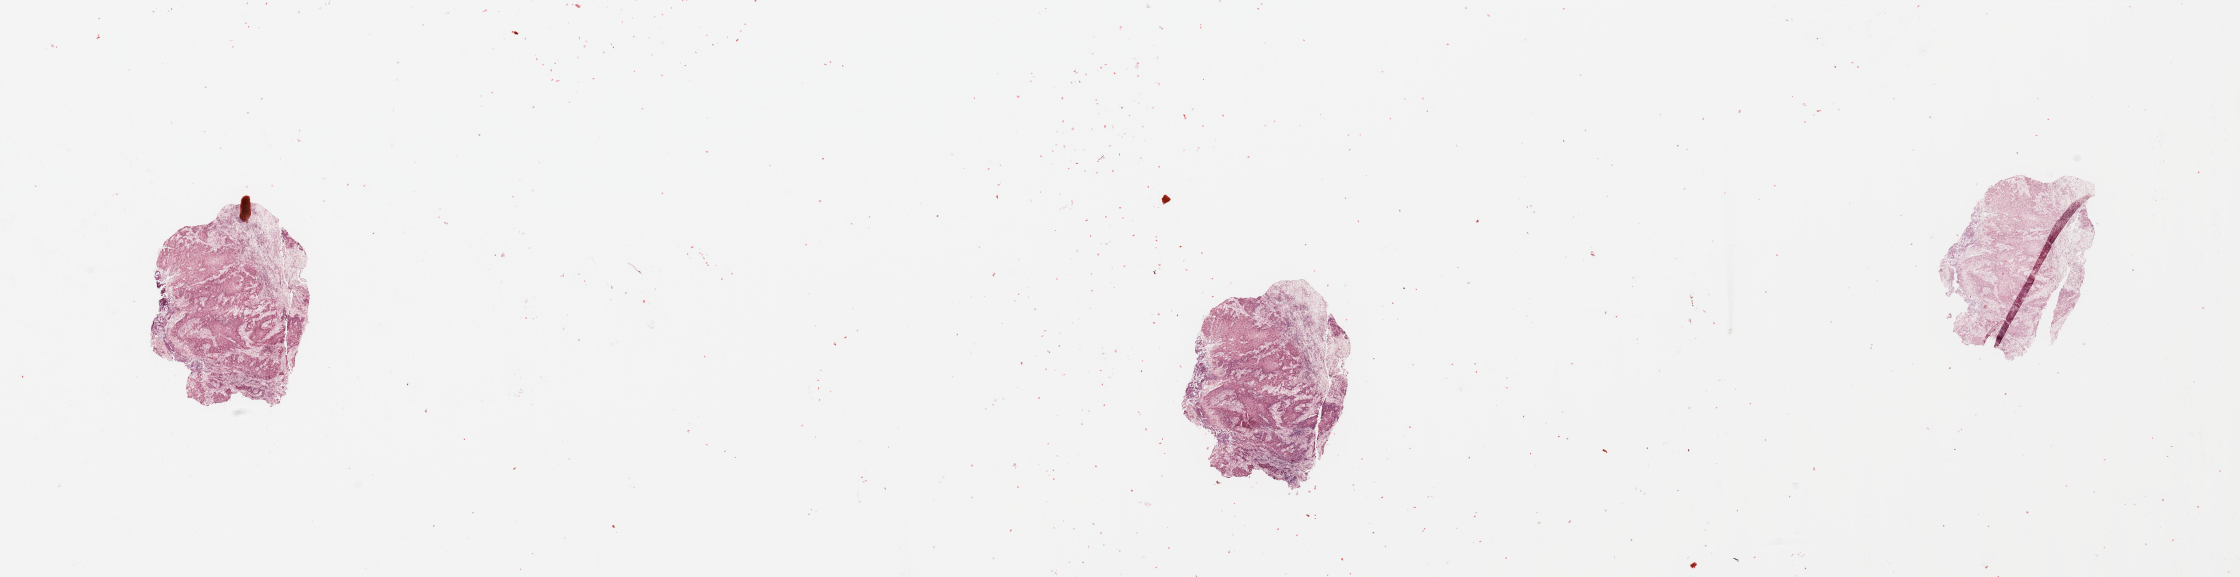
Digitized H&E-stained tissue section (whole slide), a low-resolution overview of the entire scanned area, about 35.4 x 9.1 mm (acquisition: 20x scan); tumour tissue sample, sampled site: larynx. Patient: male, age 61 years. Histologic grade: G2 (moderately differentiated). Pathologist review of this section (percent, as recorded): tumour nuclei 80%, necrosis 5%.
- AJCC pathologic stage: III
- primary tumour site (as recorded): larynx
- histologic diagnosis: Squamous cell carcinoma, NOS (larynx, NOS)